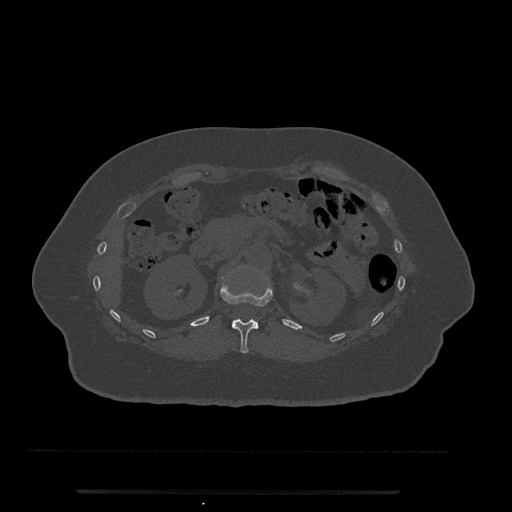
CT including the spine, one axial slice. Slice 151 of 797 in the series (ordered by position). Reconstruction kernel Br40s/3. 120 kVp. Bone window (W 1800 / L 400 HU). 0.5 mm slice thickness. 512 × 512 image matrix, field of view 440 × 440 mm. Female patient, age 51 years. From the clinical record (not read from this slice): primary cancer: neuro; vertebrae with lytic lesions (as recorded): T8.
Annotated regions visible in this slice (semi-automatic segmentation, software-assisted and operator-edited):
- T12 vertebra: bounding box (x1, y1, x2, y2) in pixels: (220, 282, 273, 354)